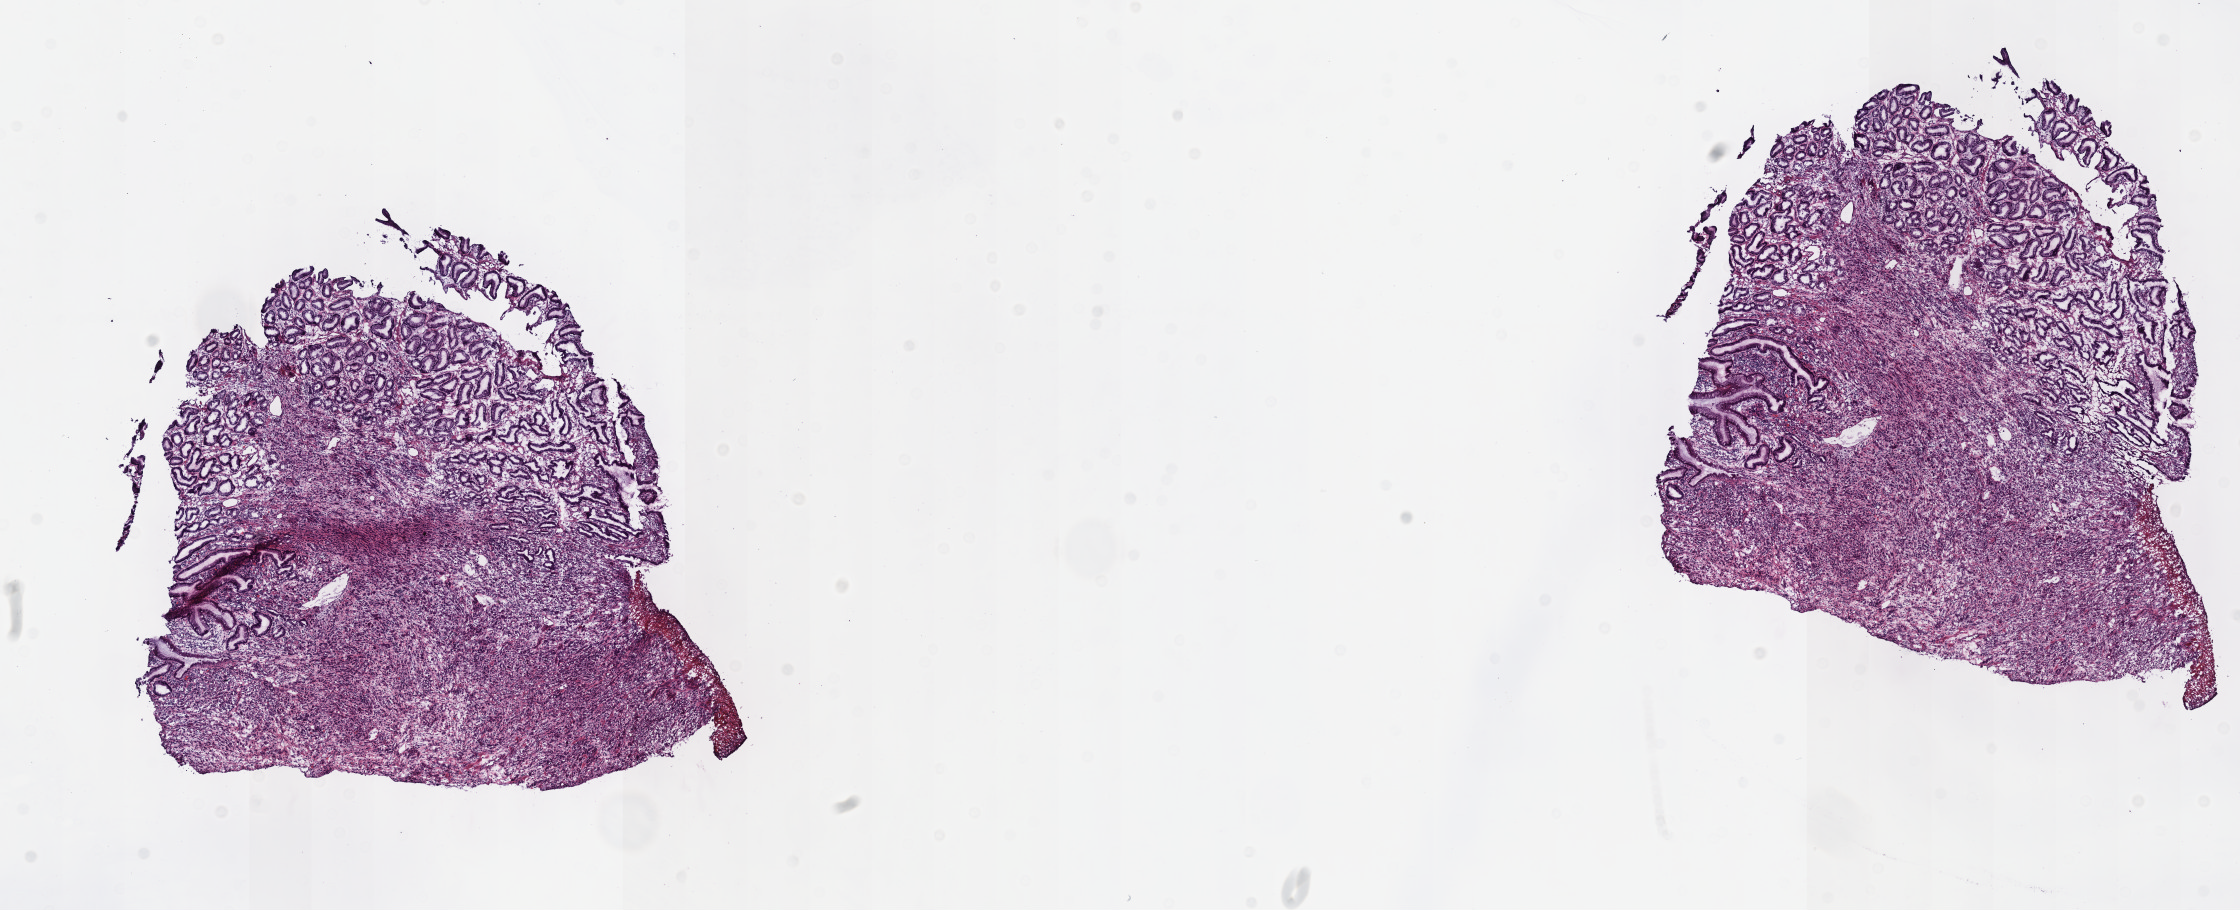
Whole-slide histology image, H&E-stained — a low-resolution overview of the entire scanned area, about 18.1 x 7.4 mm (from a 40x scan); frozen section from the top of the tissue portion; sample: primary tumour, stomach. Male patient; age at initial diagnosis 81 years. Histologic grade: G1 (well differentiated). Composition of this section per pathologist review: tumour cells 50%, tumour nuclei 60%, normal cells 25%, stromal cells 25%, necrosis 0%. Infiltration values recorded for this section: lymphocyte infiltration 80%, monocyte infiltration 20%, neutrophil infiltration 0%.
Lymph nodes positive (case pathology): 27 of 27 examined. Histologic diagnosis: Carcinoma, diffuse type (body of stomach). TNM: T3 N3 M0. AJCC pathologic stage: IIIB (7th edition).